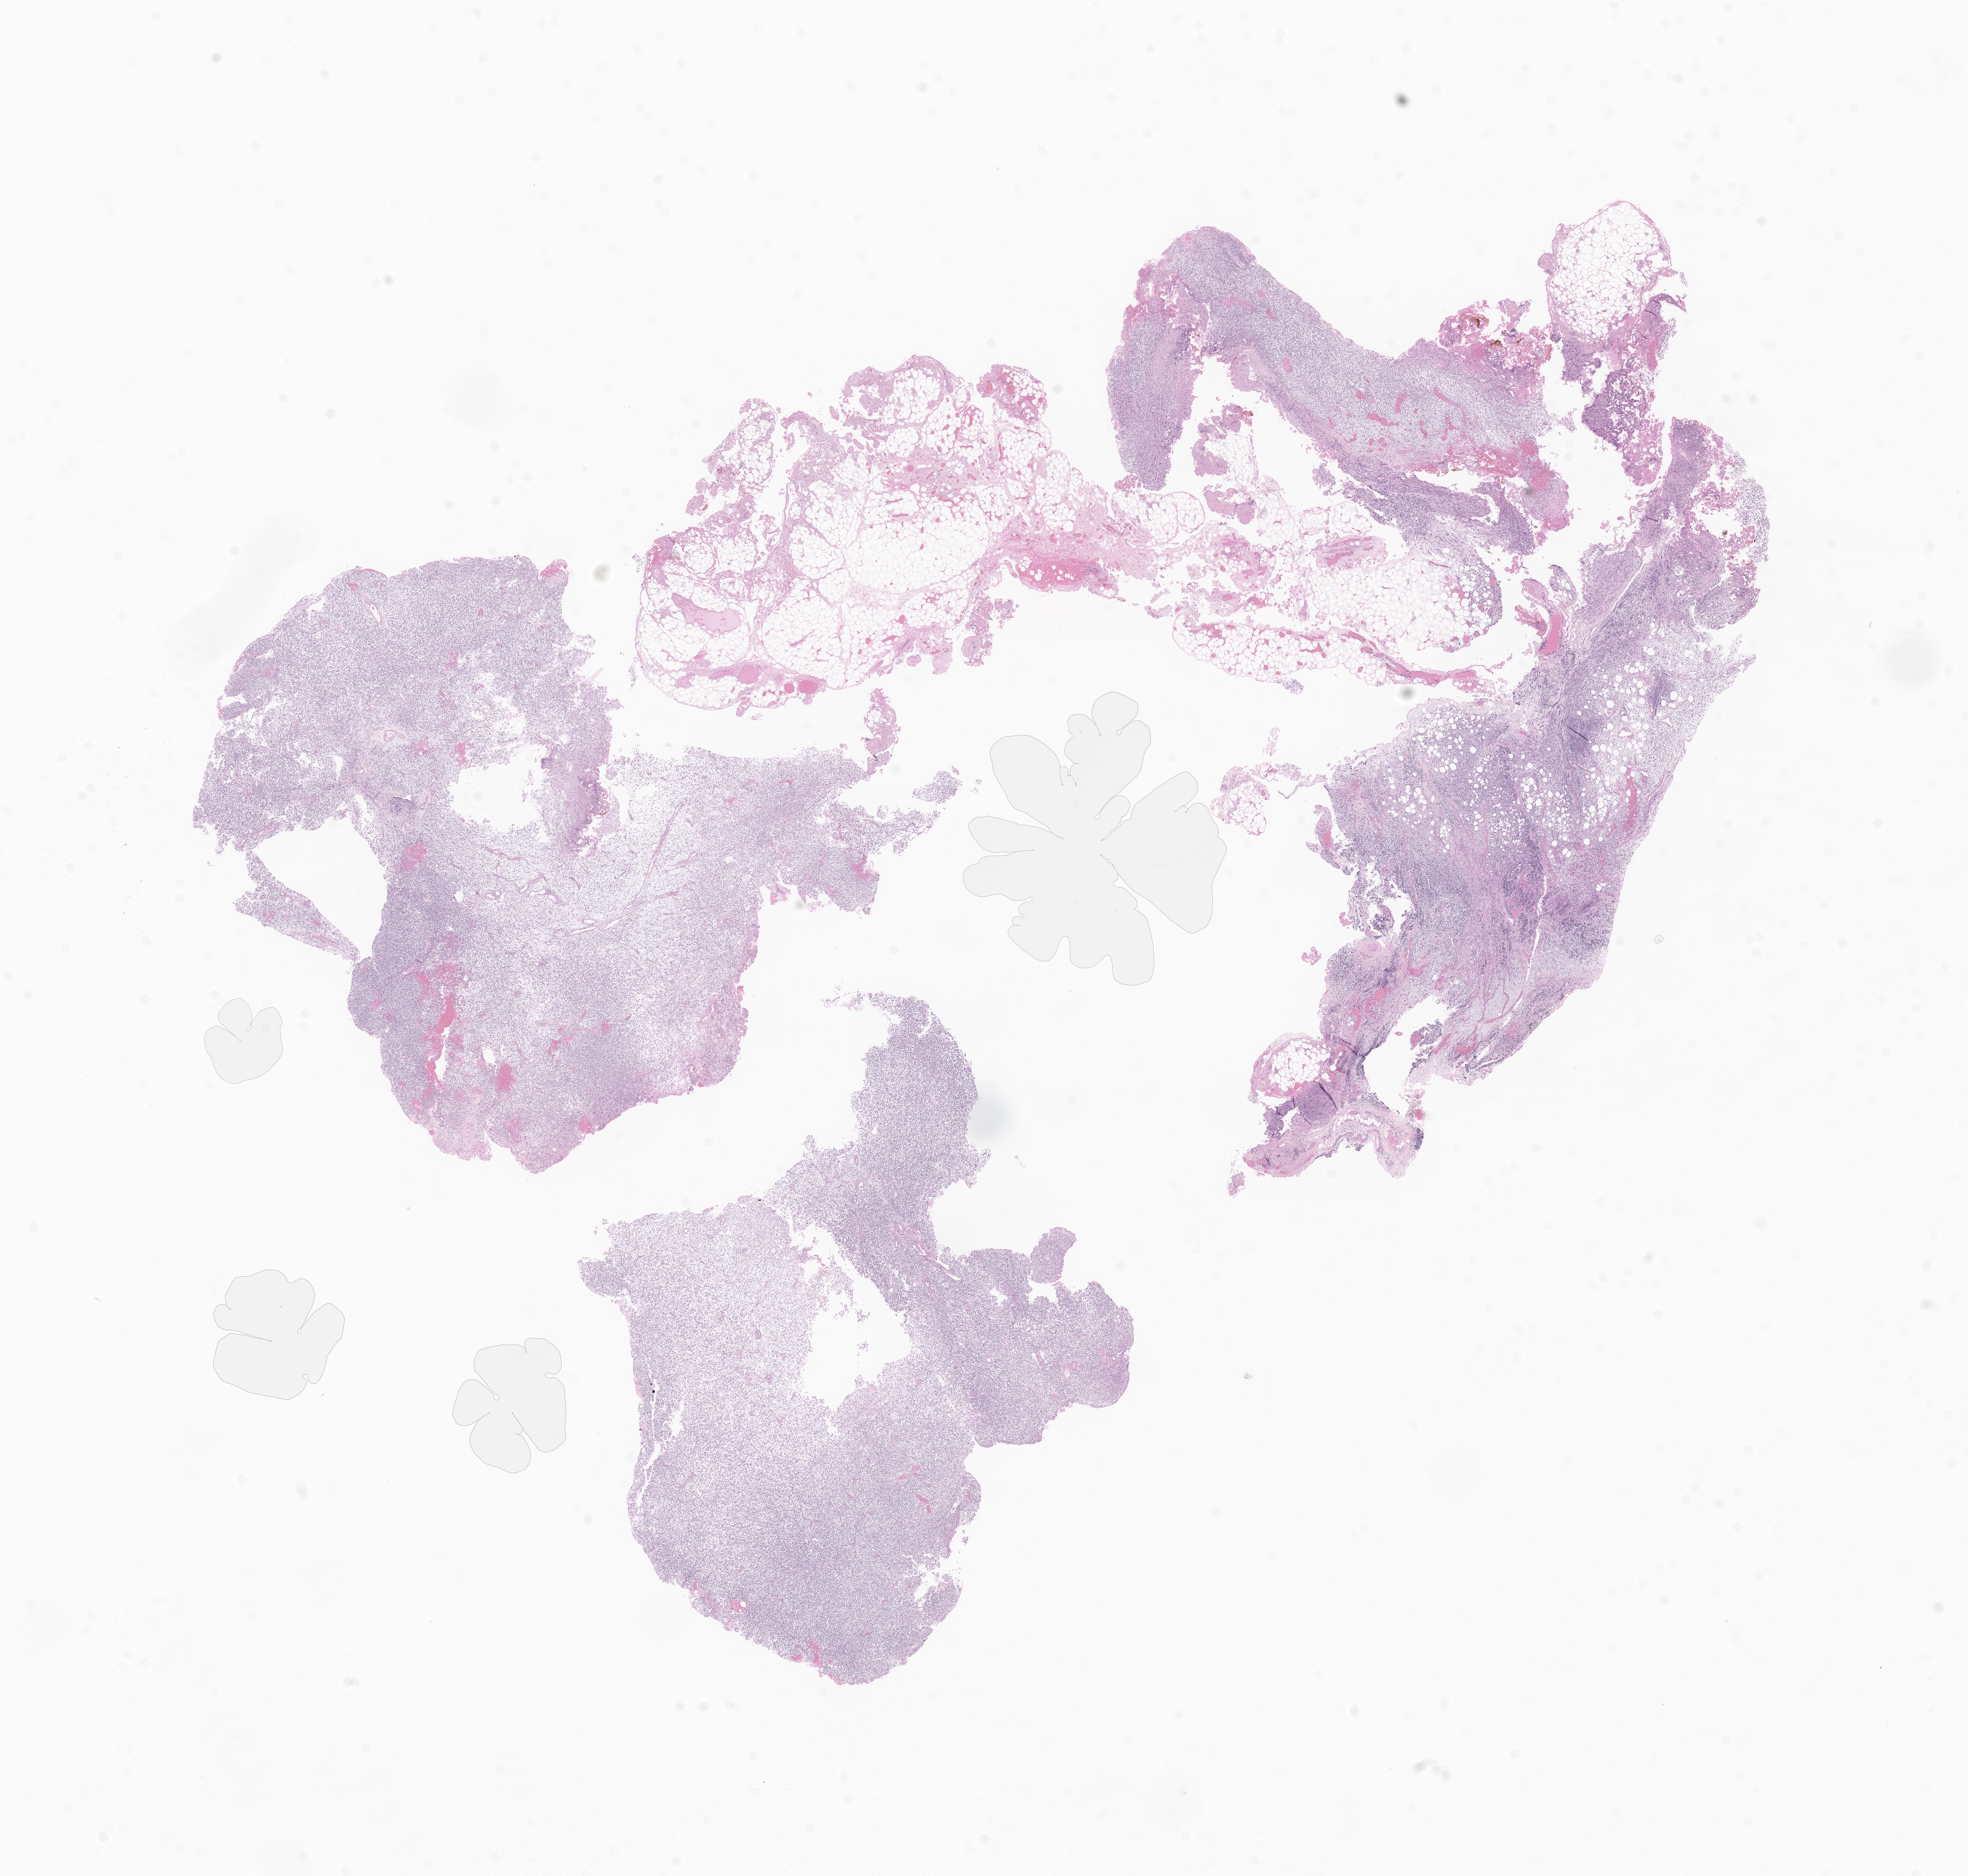
Whole-slide image, hematoxylin and eosin (H&E) stain of tumor tissue from the orbit, a low-resolution overview of the entire scanned area, about 18.6 x 17.7 mm. FFPE section. Patient female; age 176 months (14 years 8 months).
Diagnosis (ICD-O-3 morphology term): Embryonal rhabdomyosarcoma, NOS.